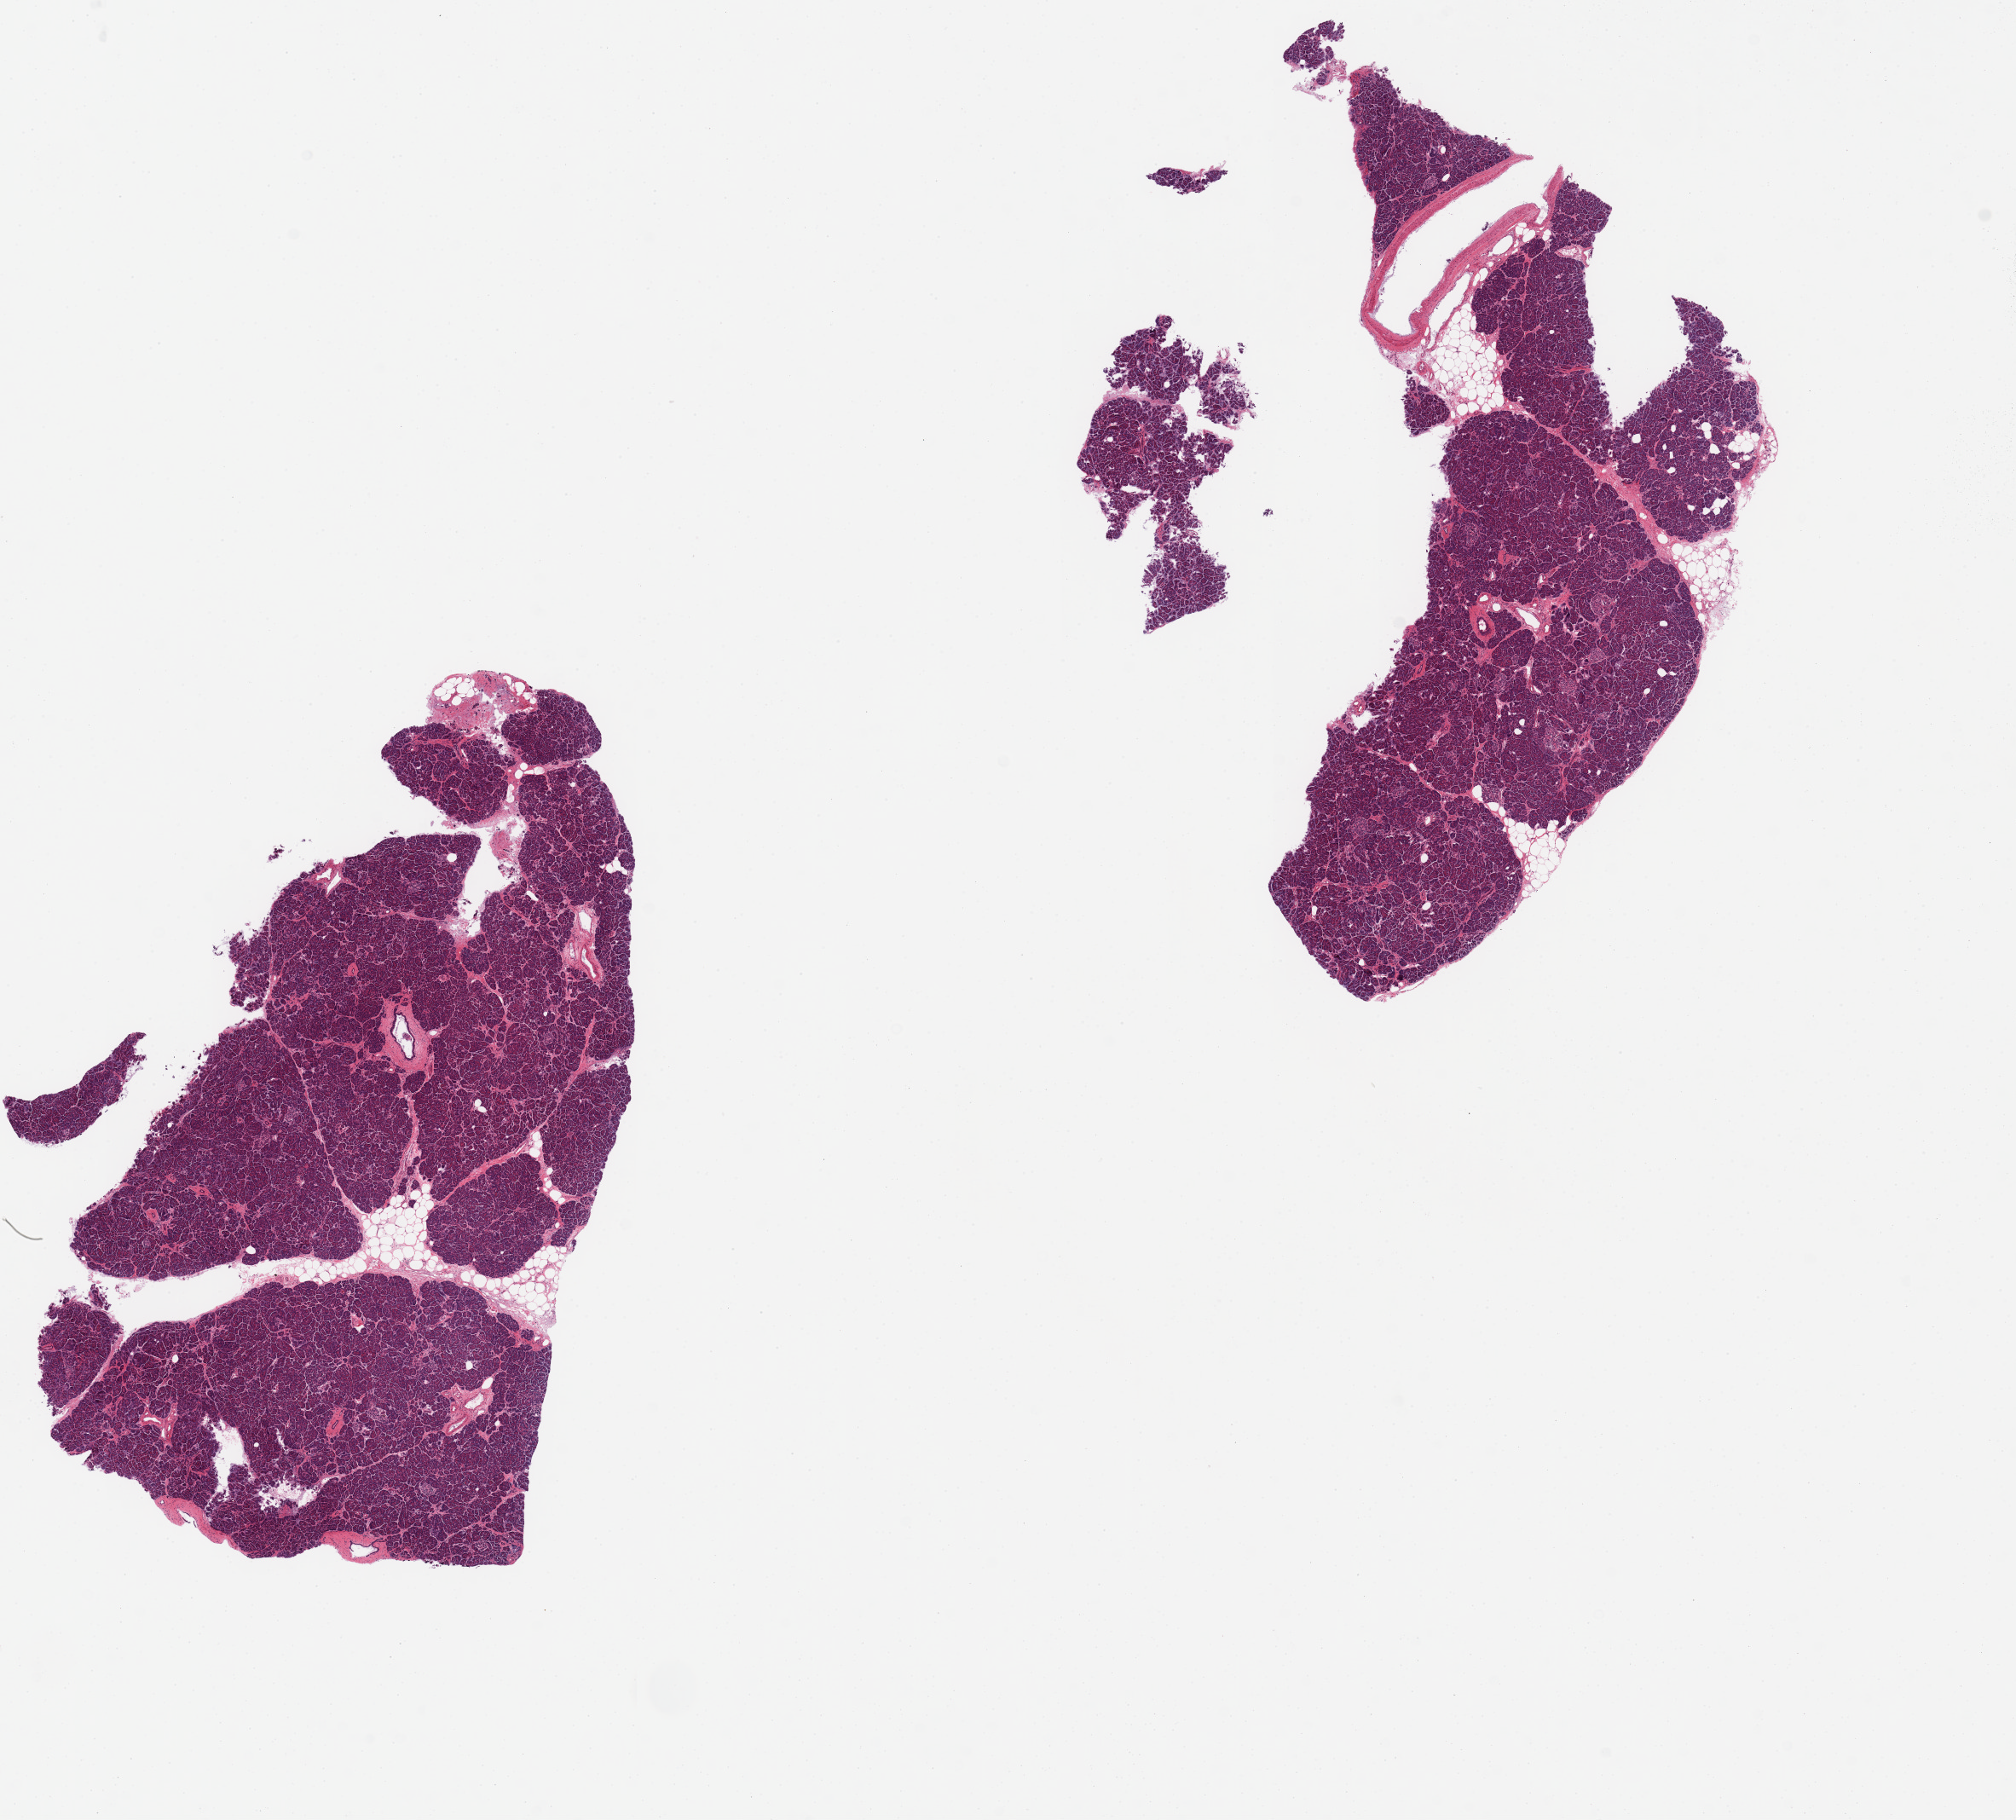
Digitized H&E-stained section, shown as a low-resolution overview of the whole scanned area (about 18.7 x 16.9 mm); PAXgene-fixed, paraffin-embedded tissue; section of pancreas (target tissue); donor tissue sample. Donor sex: male.
Reviewer comment on this tissue sample: 2 somewhat fragmented pieces.